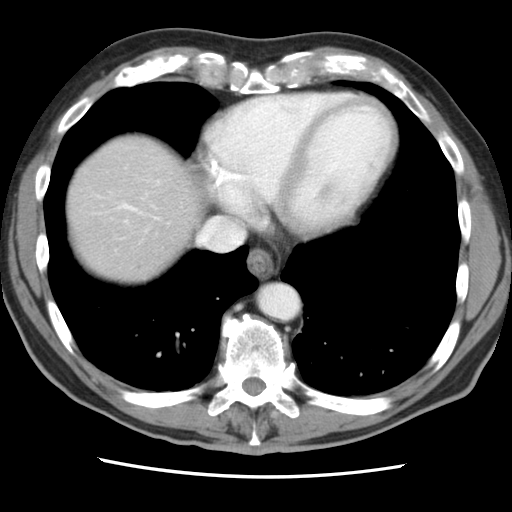
Contrast-enhanced abdominal CT, one axial slice; position 78 of 83 along the scan axis; intravenous contrast given; soft-tissue window (W 400 / L 40 HU); 512 × 512 image matrix, field of view 321 × 321 mm. Male patient, age 69 years. Case-level facts recorded for this patient, not image findings: diagnosis: colorectal cancer liver metastases, imaged before liver resection; multiple liver metastases: yes; largest metastasis: 3.5 cm; disease in both lobes: no.
Annotated regions visible in this slice (outlined manually by an expert reader):
- hepatic veins: box from (x=117, y=203) to (x=244, y=251) px
- liver: (x=67, y=134)–(x=201, y=280)
- planned liver remnant (the part of the liver to remain after resection): (x=68, y=154)–(x=201, y=281)